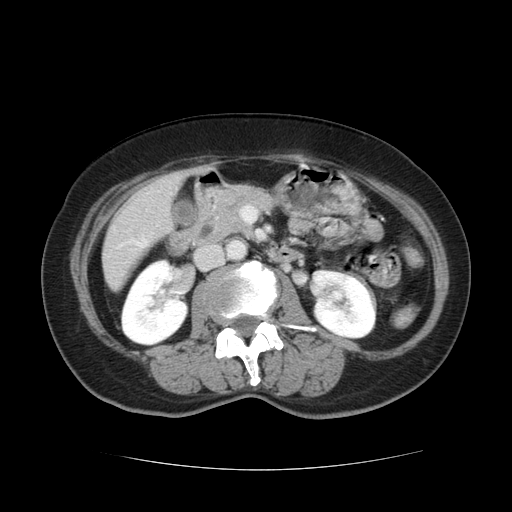
Contrast-enhanced abdominal CT, one axial slice. 120 kVp. Intravenous contrast given. Soft-tissue window (W 400 / L 40 HU). 2.5 mm slice thickness. 512 × 512 image matrix, field of view 366 × 366 mm. Female patient, age 67 years. Case-level facts recorded for this patient, not image findings: diagnosis: colorectal cancer liver metastases, imaged before liver resection; multiple liver metastases: yes; largest metastasis: 3 cm.
Outlined on this slice (outlined manually by an expert reader):
- liver: bounding box (x1, y1, x2, y2) in pixels: (103, 174, 181, 288)
- planned liver remnant (the part of the liver to remain after resection): (103, 218, 146, 288)